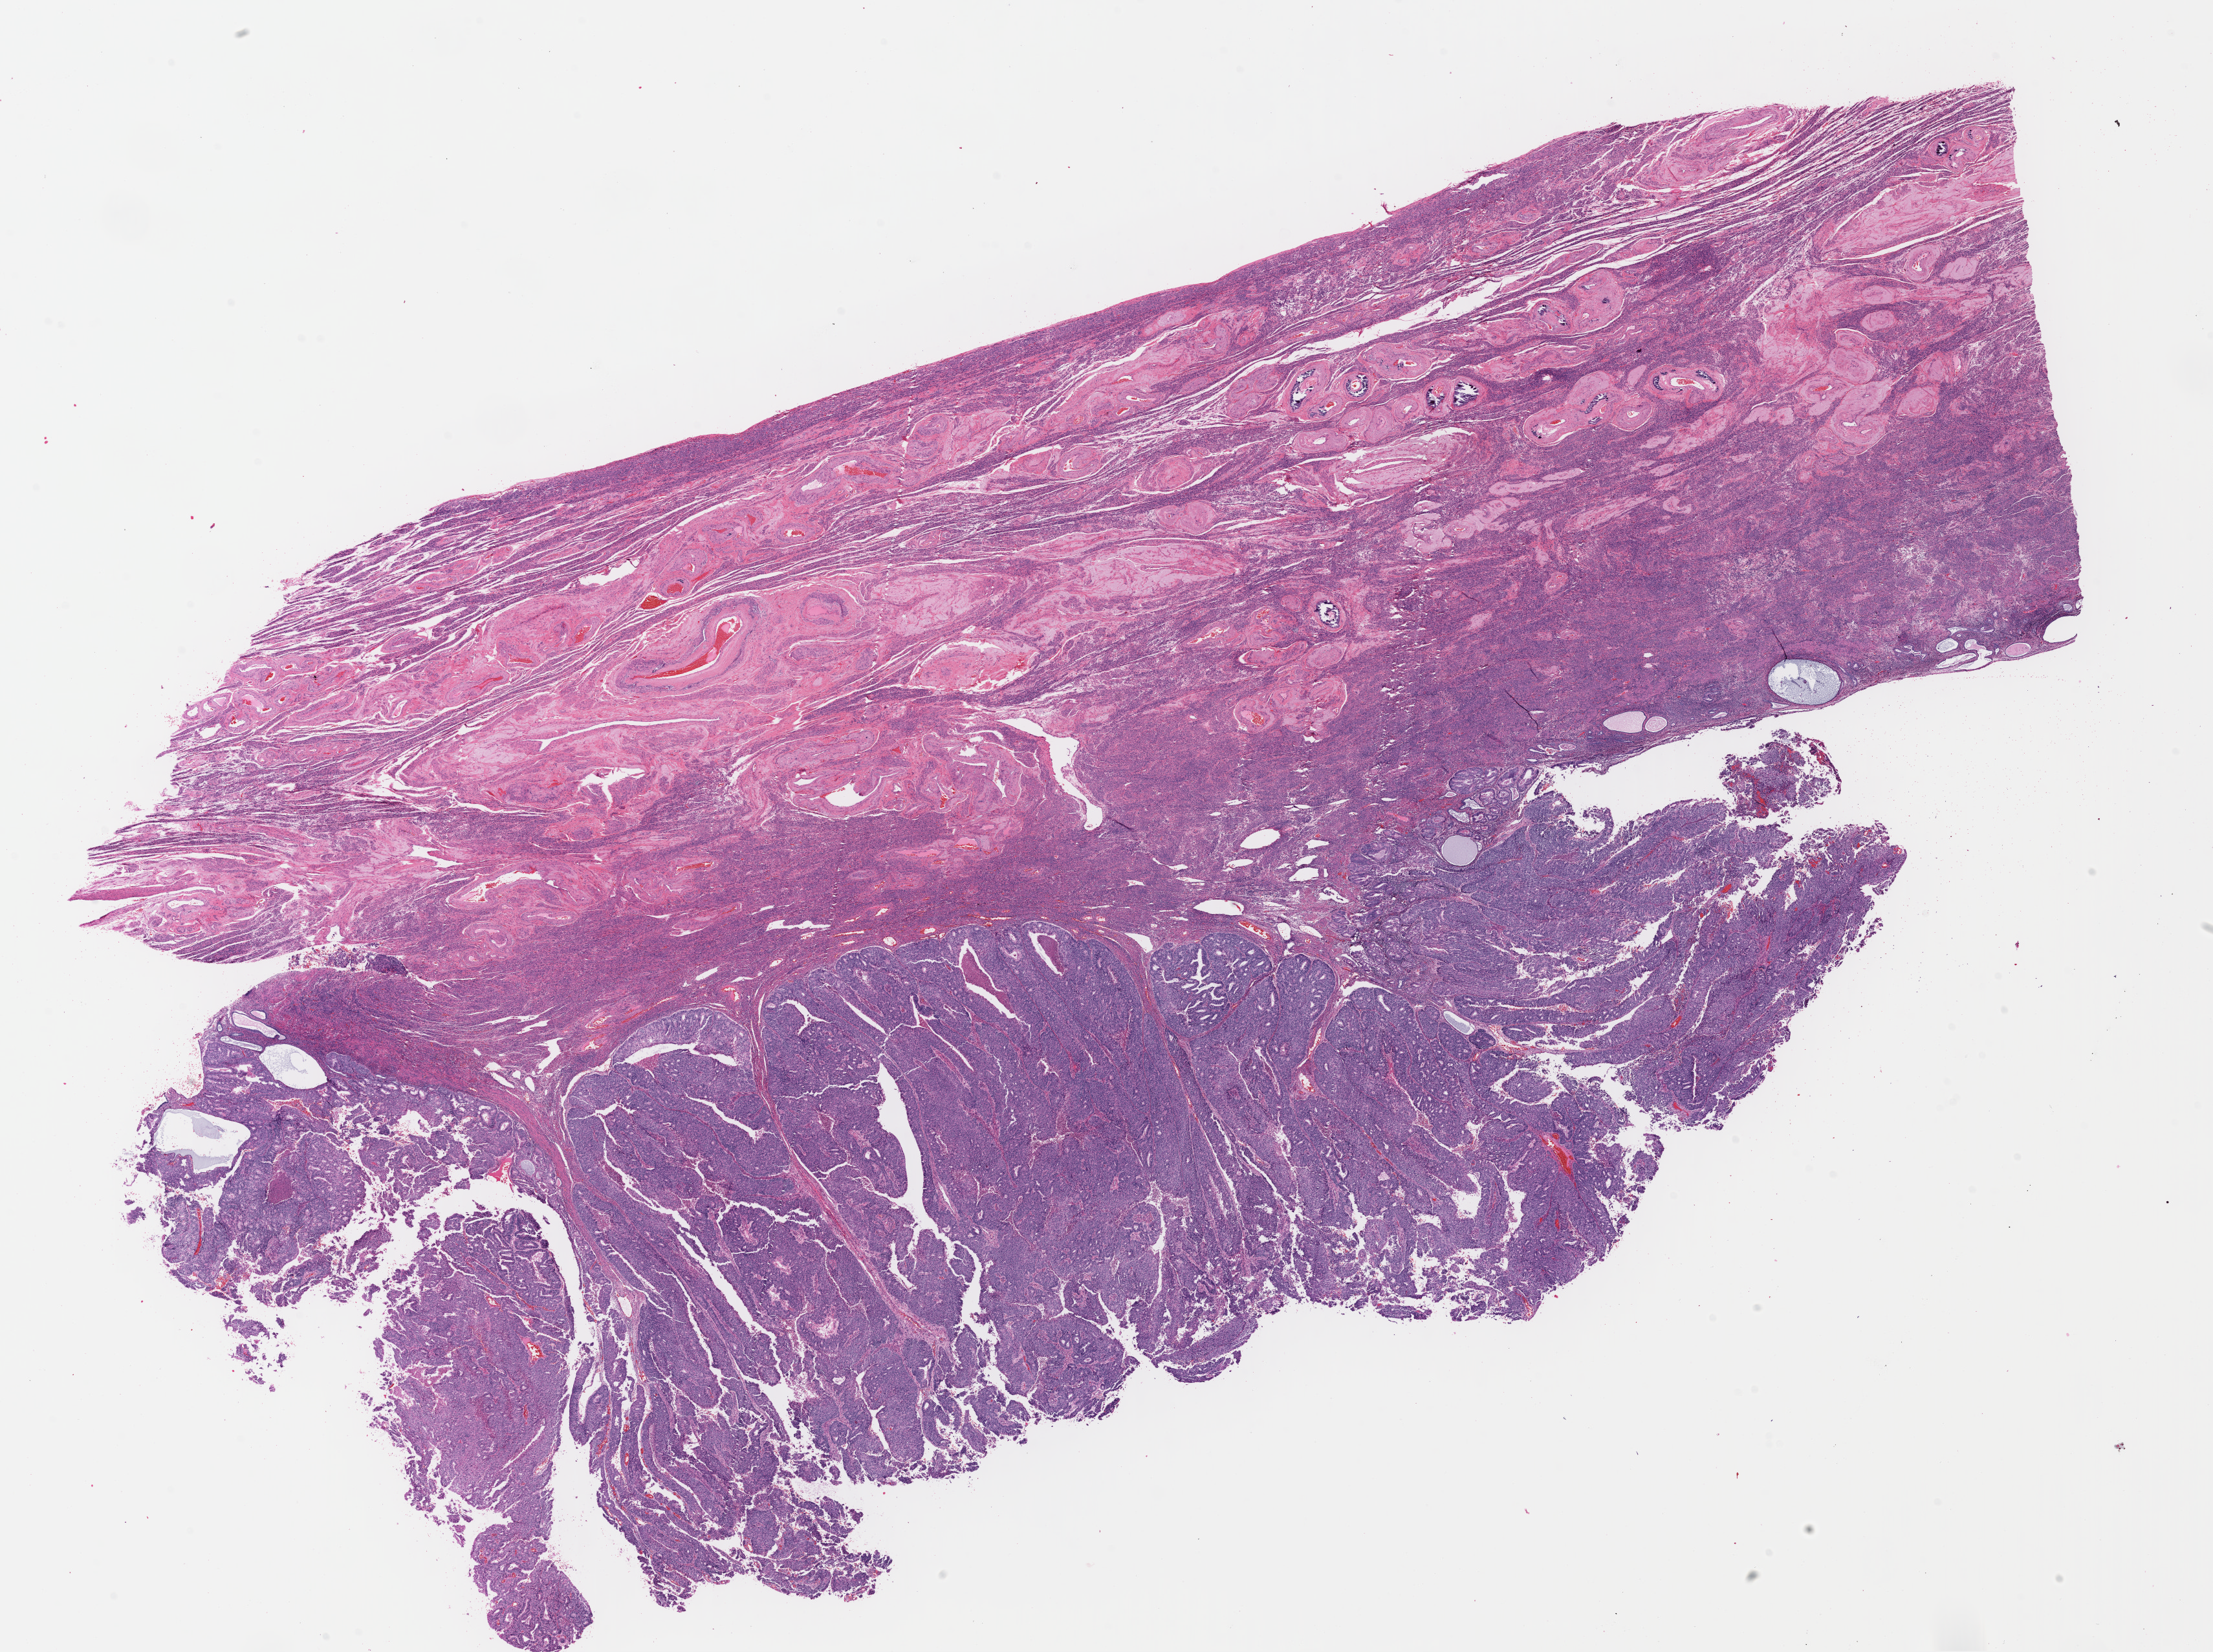
Whole-slide histology image, H&E-stained, a low-resolution overview of the entire scanned area, about 26.9 x 20.1 mm; formalin-fixed paraffin-embedded (FFPE) diagnostic section; uterus, primary tumour sample. Patient sex: female. Histologic grade: G3 (poorly differentiated).
FIGO stage: IB. Histologic diagnosis: Endometrioid adenocarcinoma, NOS (endometrium).